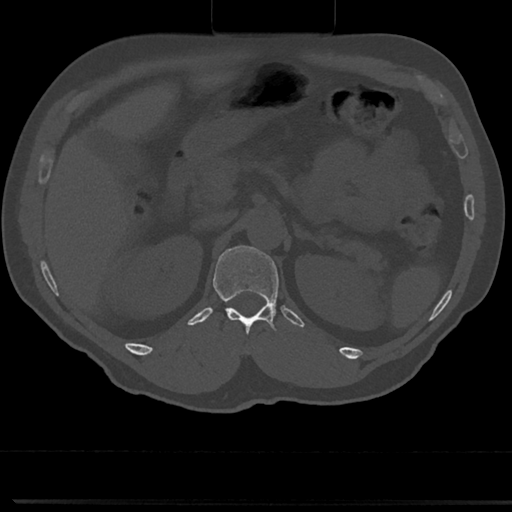
CT including the spine, one axial slice. Position 139 of 817 along the scan axis. Reconstruction kernel Br40s/3. Bone window (W 1800 / L 400 HU). 0.5 mm slice thickness. 512 × 512 image matrix. Patient: male, 61 years. Case-level facts recorded for this patient, not image findings: primary cancer: prostate.
Structures marked on this image (semi-automatically segmented with operator editing):
- T12 vertebra: bounding box <212,254,282,356> (left, top, right, bottom; pixels)